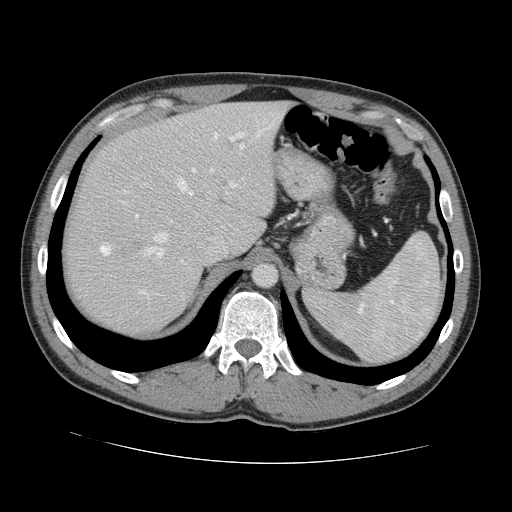
Contrast-enhanced abdominal CT, one axial slice. Slice 100 of 131 in the series (ordered by position). 120 kVp. Intravenous contrast given. Soft-tissue window (W 400 / L 40 HU). 512 × 512 image matrix. Male patient, age 40 years. Case-level facts recorded for this patient, not image findings: diagnosis: colorectal cancer liver metastases, imaged before liver resection; multiple liver metastases: yes; largest metastasis: 2.9 cm; disease in both lobes: yes.
Outlined on this slice (outlined manually by an expert reader):
- hepatic veins: bounding box (x1, y1, x2, y2) in pixels: (146, 136, 243, 257)
- liver: (65, 102, 286, 334)
- planned liver remnant (the part of the liver to remain after resection): (97, 102, 286, 252)
- portal vein (with intrahepatic branches): (192, 132, 245, 188)